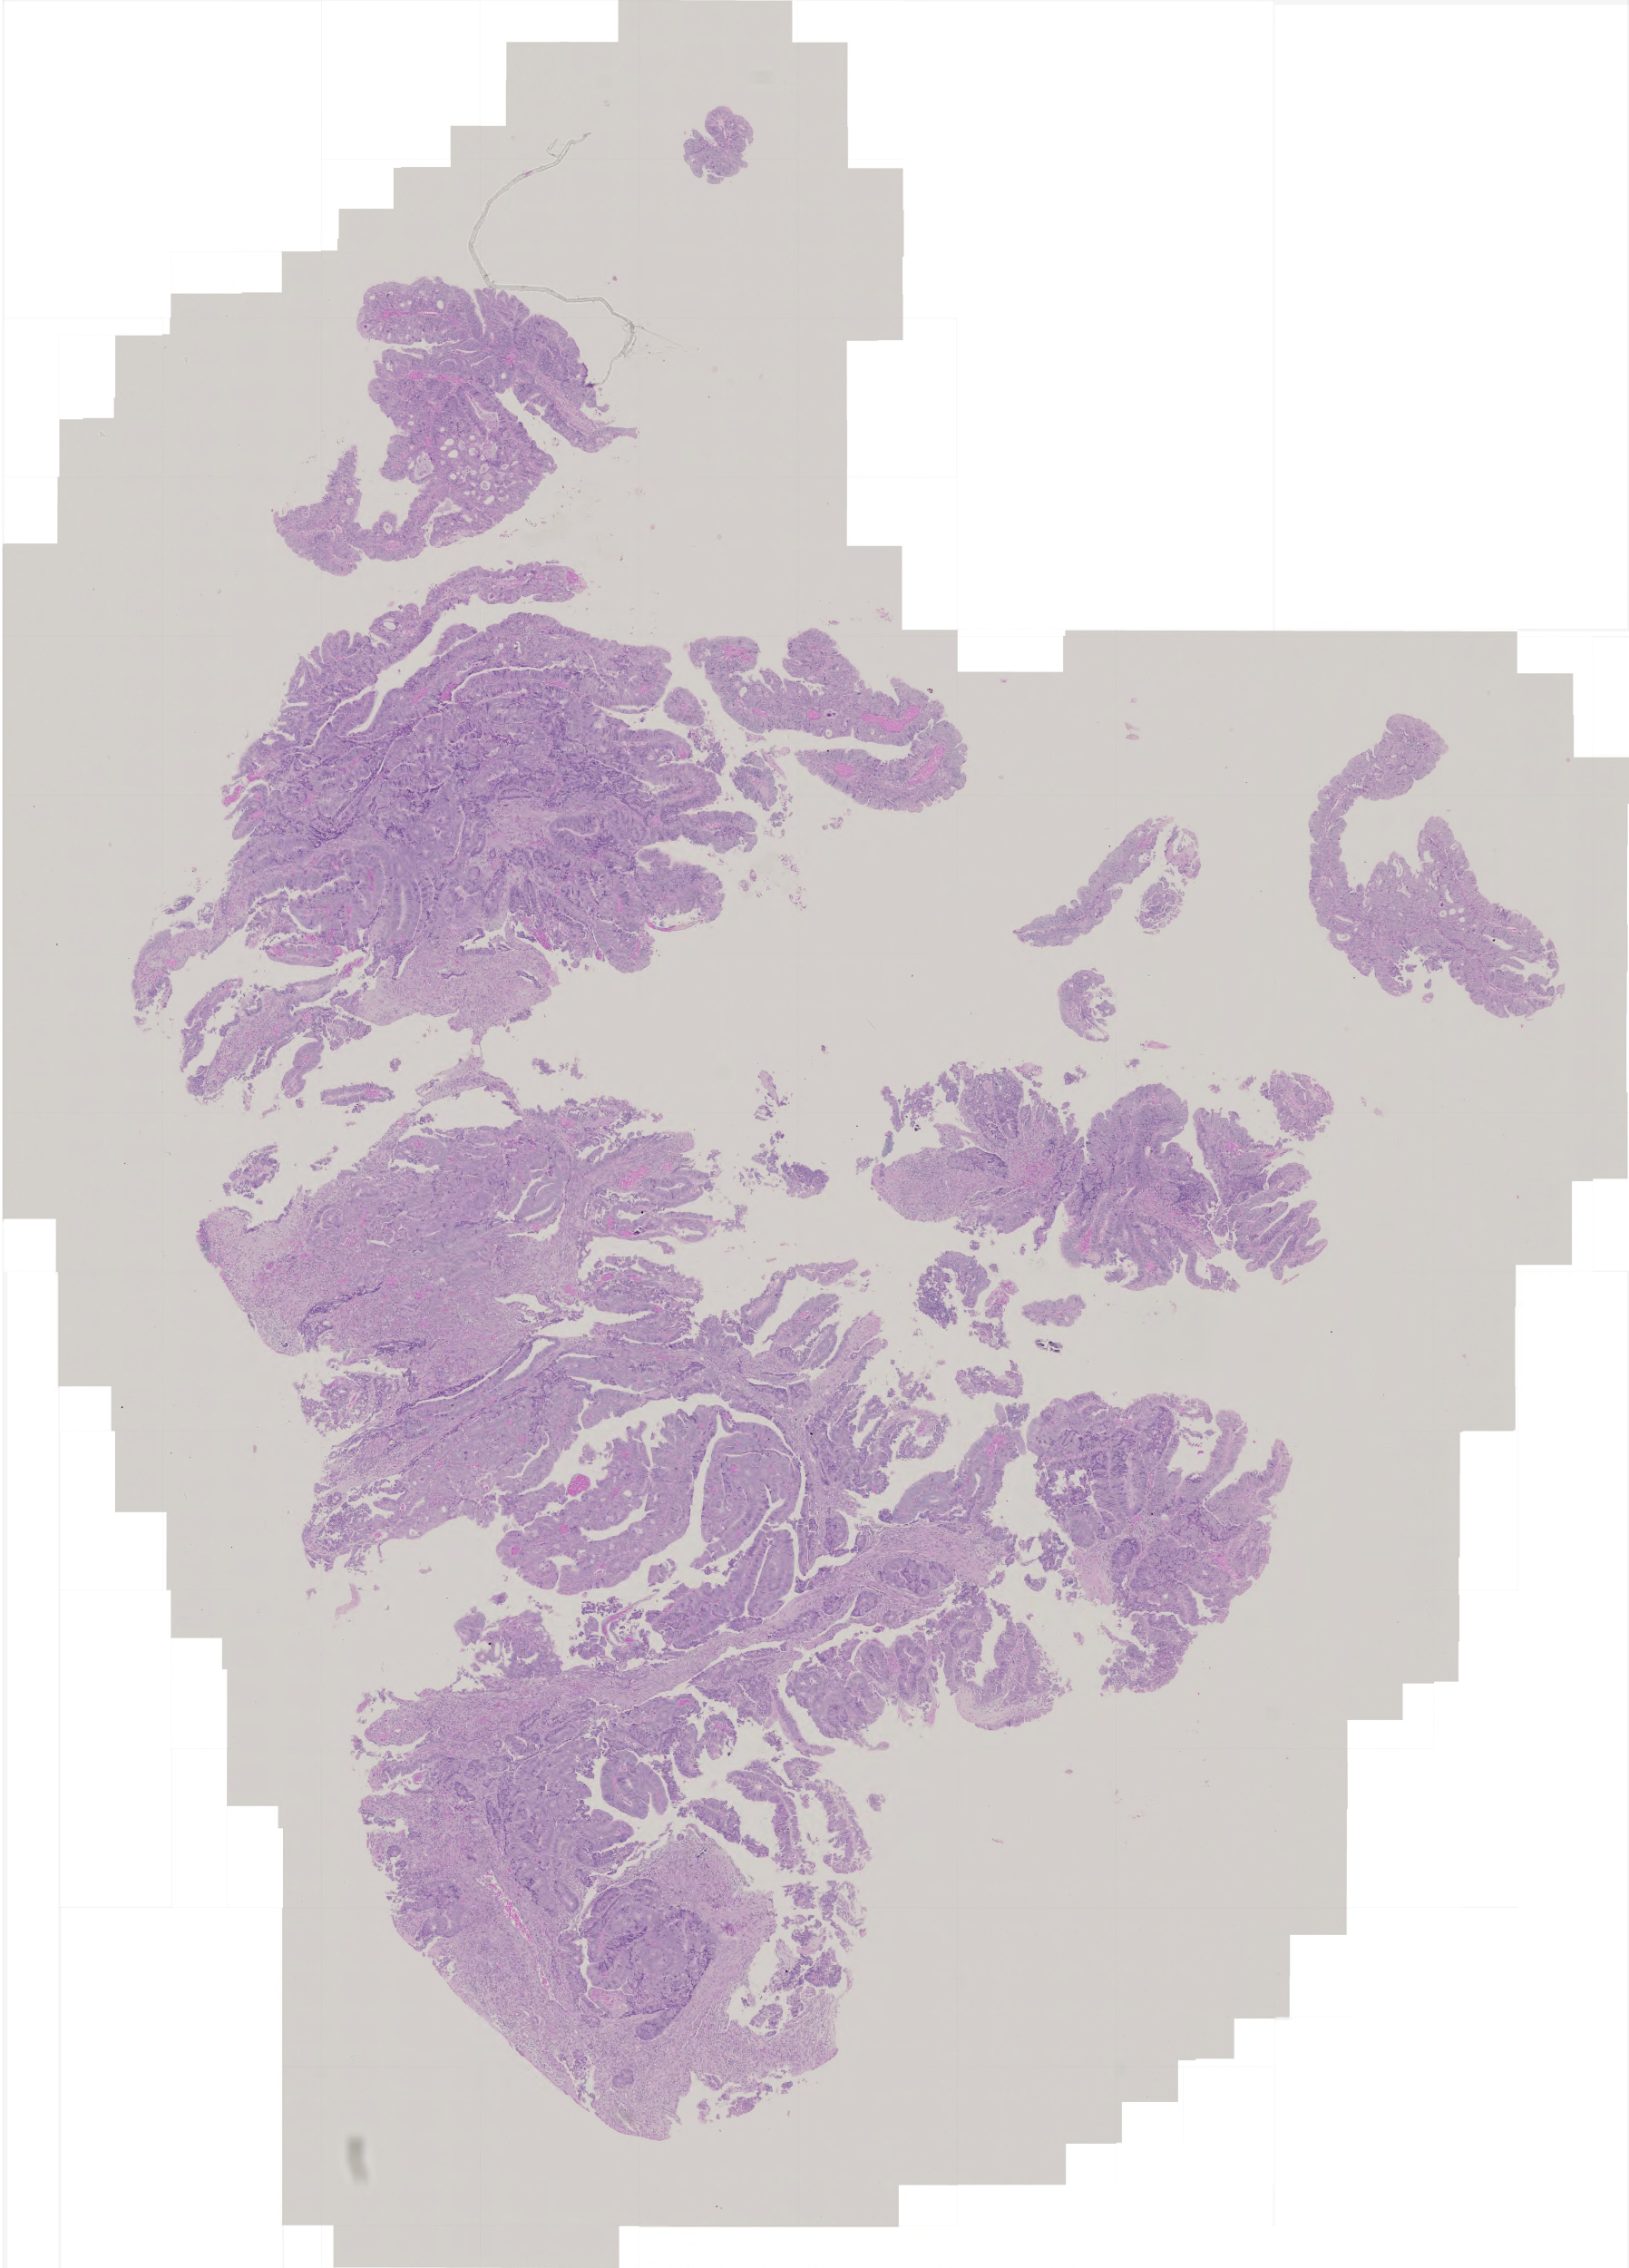
Digitized H&E tissue section (whole slide) — a low-resolution overview of the entire scanned area, about 3.6 x 5.0 mm. FFPE section. Primary tumour sample from the rectum. Female, age 85 years at initial diagnosis.
* pathologic diagnosis: Adenocarcinoma, NOS
* AJCC pathologic stage: I (5th edition)